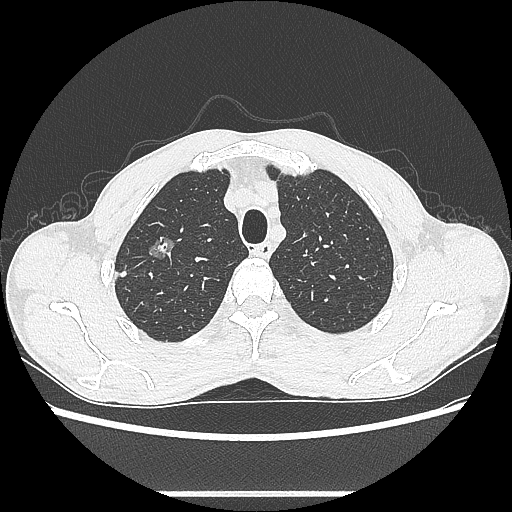
Chest CT, one axial slice. Lung window (W 1500 / L -600 HU). 512 × 512 image matrix, field of view 357 × 357 mm. Male patient, age 54 years. From the clinical record (not read from this slice): clinical TNM (as recorded): T1a N0 M0.
Annotated regions visible in this slice (bounding box drawn by a radiologist):
- lung tumour (recorded histology: adenocarcinoma): bounding box <142,225,181,269> (left, top, right, bottom; pixels)